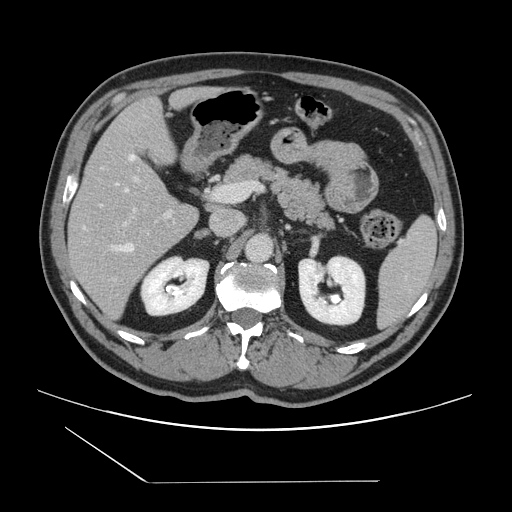
Contrast-enhanced abdominal CT, one axial slice. Position 77 of 157 along the scan axis. 120 kVp. Intravenous contrast given. Soft-tissue window (W 400 / L 40 HU). 2.5 mm slice thickness. 512 × 512 image matrix, field of view 407 × 407 mm. Male patient, age 61 years. From the clinical record (not read from this slice): diagnosis: colorectal cancer liver metastases, imaged before liver resection; multiple liver metastases: yes.
Structures marked on this image (expert manual segmentation):
- hepatic veins: bounding box [x1, y1, x2, y2] px = [83, 155, 135, 252]
- liver: [69, 89, 209, 326]
- planned liver remnant (the part of the liver to remain after resection): [71, 88, 209, 220]
- portal vein (with intrahepatic branches): [100, 177, 172, 225]